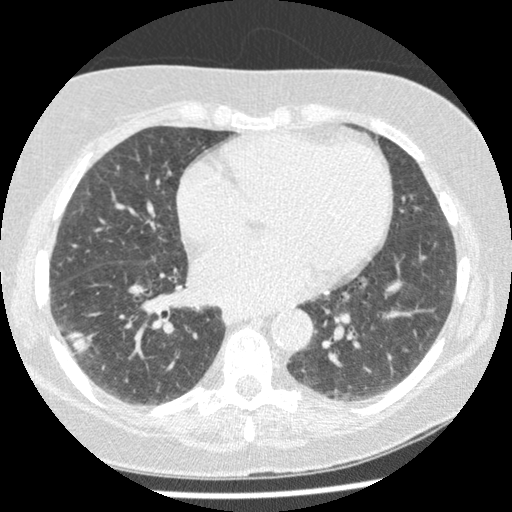
Low-dose screening chest CT, one axial slice; slice 104 of 241 in the series (ordered by position); reconstruction kernel STANDARD; lung window (W 1500 / L -600 HU); 1.25 mm slice thickness; 512 × 512 image matrix, field of view 305 × 305 mm.
Outlined on this slice (outlined manually by an expert reader):
- lesion 1 (tumor, lower lobe of right lung): bounding box [x1, y1, x2, y2] px = [66, 331, 90, 356]